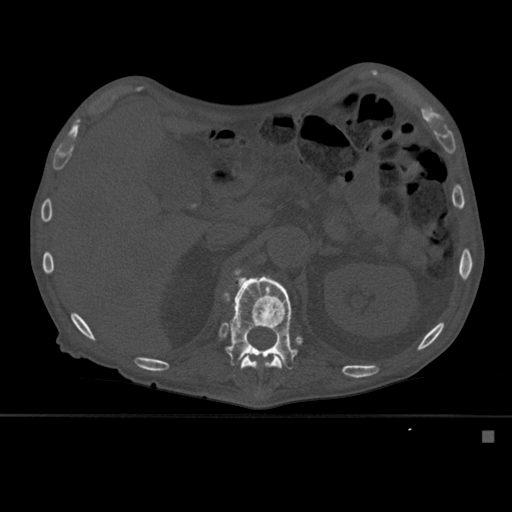
CT including the spine, one axial slice; slice 262 of 527 in the series (ordered by position); bone window (W 1800 / L 400 HU); 512 × 512 image matrix, field of view 373 × 373 mm. Male patient, age 78 years. Case-level facts recorded for this patient, not image findings: primary cancer: prostate.
Outlined on this slice (semi-automatic segmentation, software-assisted and operator-edited):
- L1 vertebra: bounding box (x1, y1, x2, y2) in pixels: (222, 274, 298, 396)
- T12 vertebra: (233, 268, 282, 371)